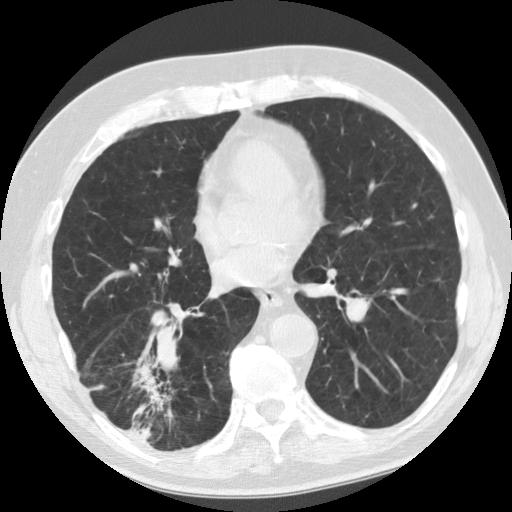
Chest CT (low-dose screening protocol), one axial image, baseline annual screen, lung window (W 1500 / L -600 HU), 2.5 mm slice thickness, slice 82 of 135 in the series. Male participant, aged 69 years at enrolment. Former smoker at enrolment.
Expert reader's lesion annotation, bounding box [x1, y1, x2, y2] px = [114, 332, 200, 442]. The screening reader recorded 2 non-calcified nodules or masses ≥4 mm on this exam (right lower lobe, right lower lobe); which of them this box marks is not recorded. Participant outcome: lung cancer diagnosed 40 days after this screen — adenocarcinoma, NOS, right lower lobe, stage IIB (AJCC 6th edition), 45 mm at pathology.